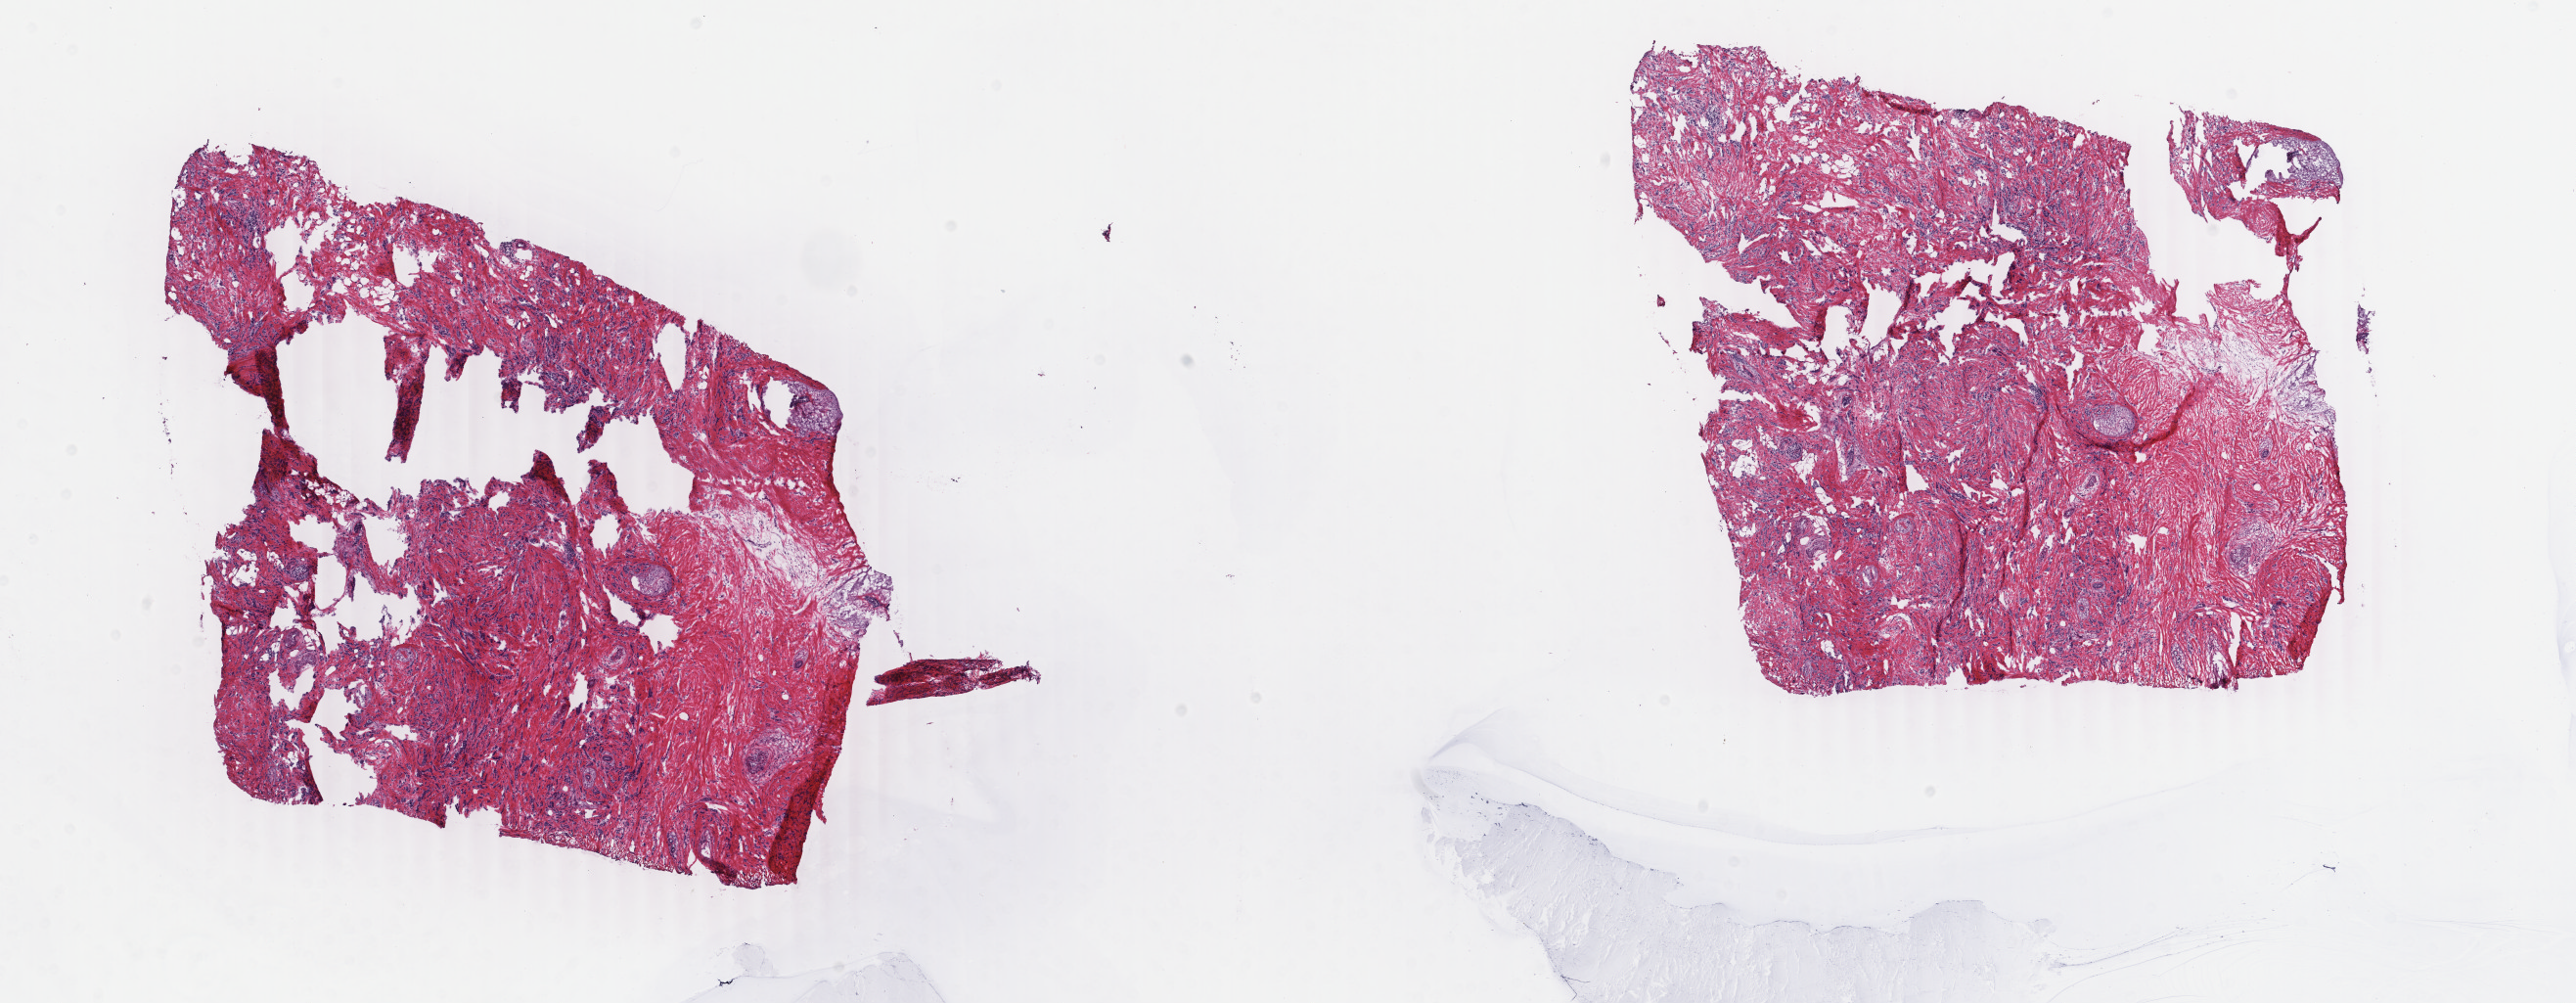
Whole-slide histology image, Hematoxylin and eosin (H&E) stained — low-resolution overview of the scanned area, about 20.9 x 8.2 mm (acquisition: 40x scan); frozen section from the bottom of the tissue portion; primary tumour sample from the breast. Female patient; age at initial diagnosis 80 years. Slide review estimates, as recorded: tumour cells 85%, tumour nuclei 75%, normal cells 0%, stromal cells 15%, necrosis 0%. Infiltration values recorded for this section: lymphocyte infiltration 0%, monocyte infiltration 0%, neutrophil infiltration 0%.
* diagnosis: Infiltrating duct carcinoma, NOS
* AJCC pathologic stage: IIA (7th edition)
* lymph nodes positive (case pathology): 1 of 7 examined